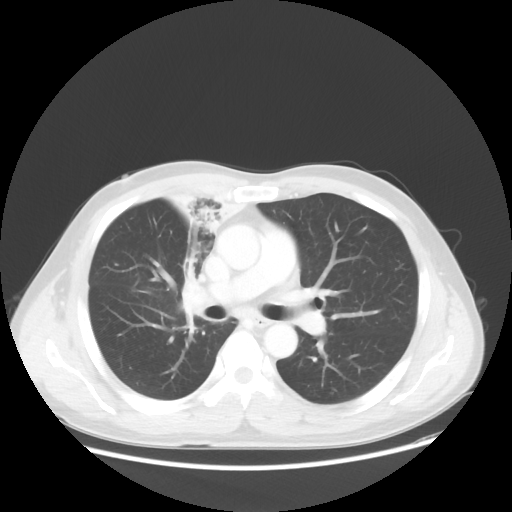
Chest CT, one axial slice. Position 32 of 56 along the scan axis. Reconstruction kernel STANDARD. Lung window (W 1500 / L -600 HU). 512 × 512 image matrix, field of view 398 × 398 mm. Patient: male, 60 years. From the clinical record (not read from this slice): clinical TNM (as recorded): T2a N1 M0.
Structures marked on this image (rectangle marked by the reading radiologist):
- lung tumour (recorded histology: squamous cell carcinoma): bounding box <152,169,237,234> (left, top, right, bottom; pixels)